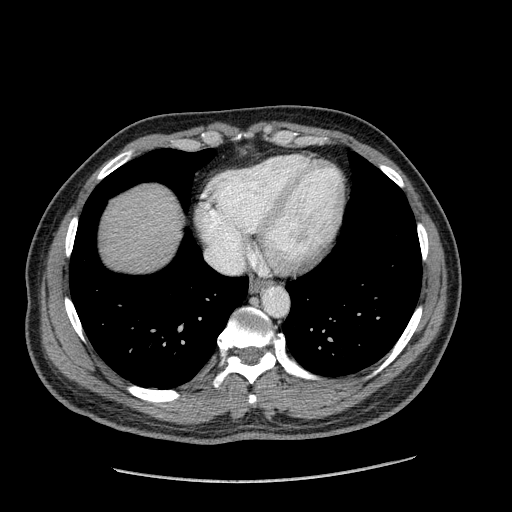
Contrast-enhanced abdominal CT (liver protocol), one axial slice. Position 169 of 182 along the scan axis. Reconstruction kernel STANDARD. 120 kVp. Soft-tissue window (W 400 / L 40 HU). 2.5 mm slice thickness. 512 × 512 image matrix, field of view 400 × 400 mm. From the clinical record (not read from this slice): diagnosis: hepatocellular carcinoma (patient treated with transarterial chemoembolisation; whether this scan precedes or follows treatment is not stated here); TNM stage (as recorded): Stage-I; Child-Pugh class: A; tumour differentiation: well differentiated; tumour nodularity: uninodular.
Annotated regions visible in this slice (semi-automatically segmented with operator editing):
- abdominal aorta: bounding box [x1, y1, x2, y2] px = [262, 287, 288, 316]
- liver parenchyma outside the tumour (the mass and vessels are separate outlines, so this box may not span the whole liver): [102, 184, 182, 272]